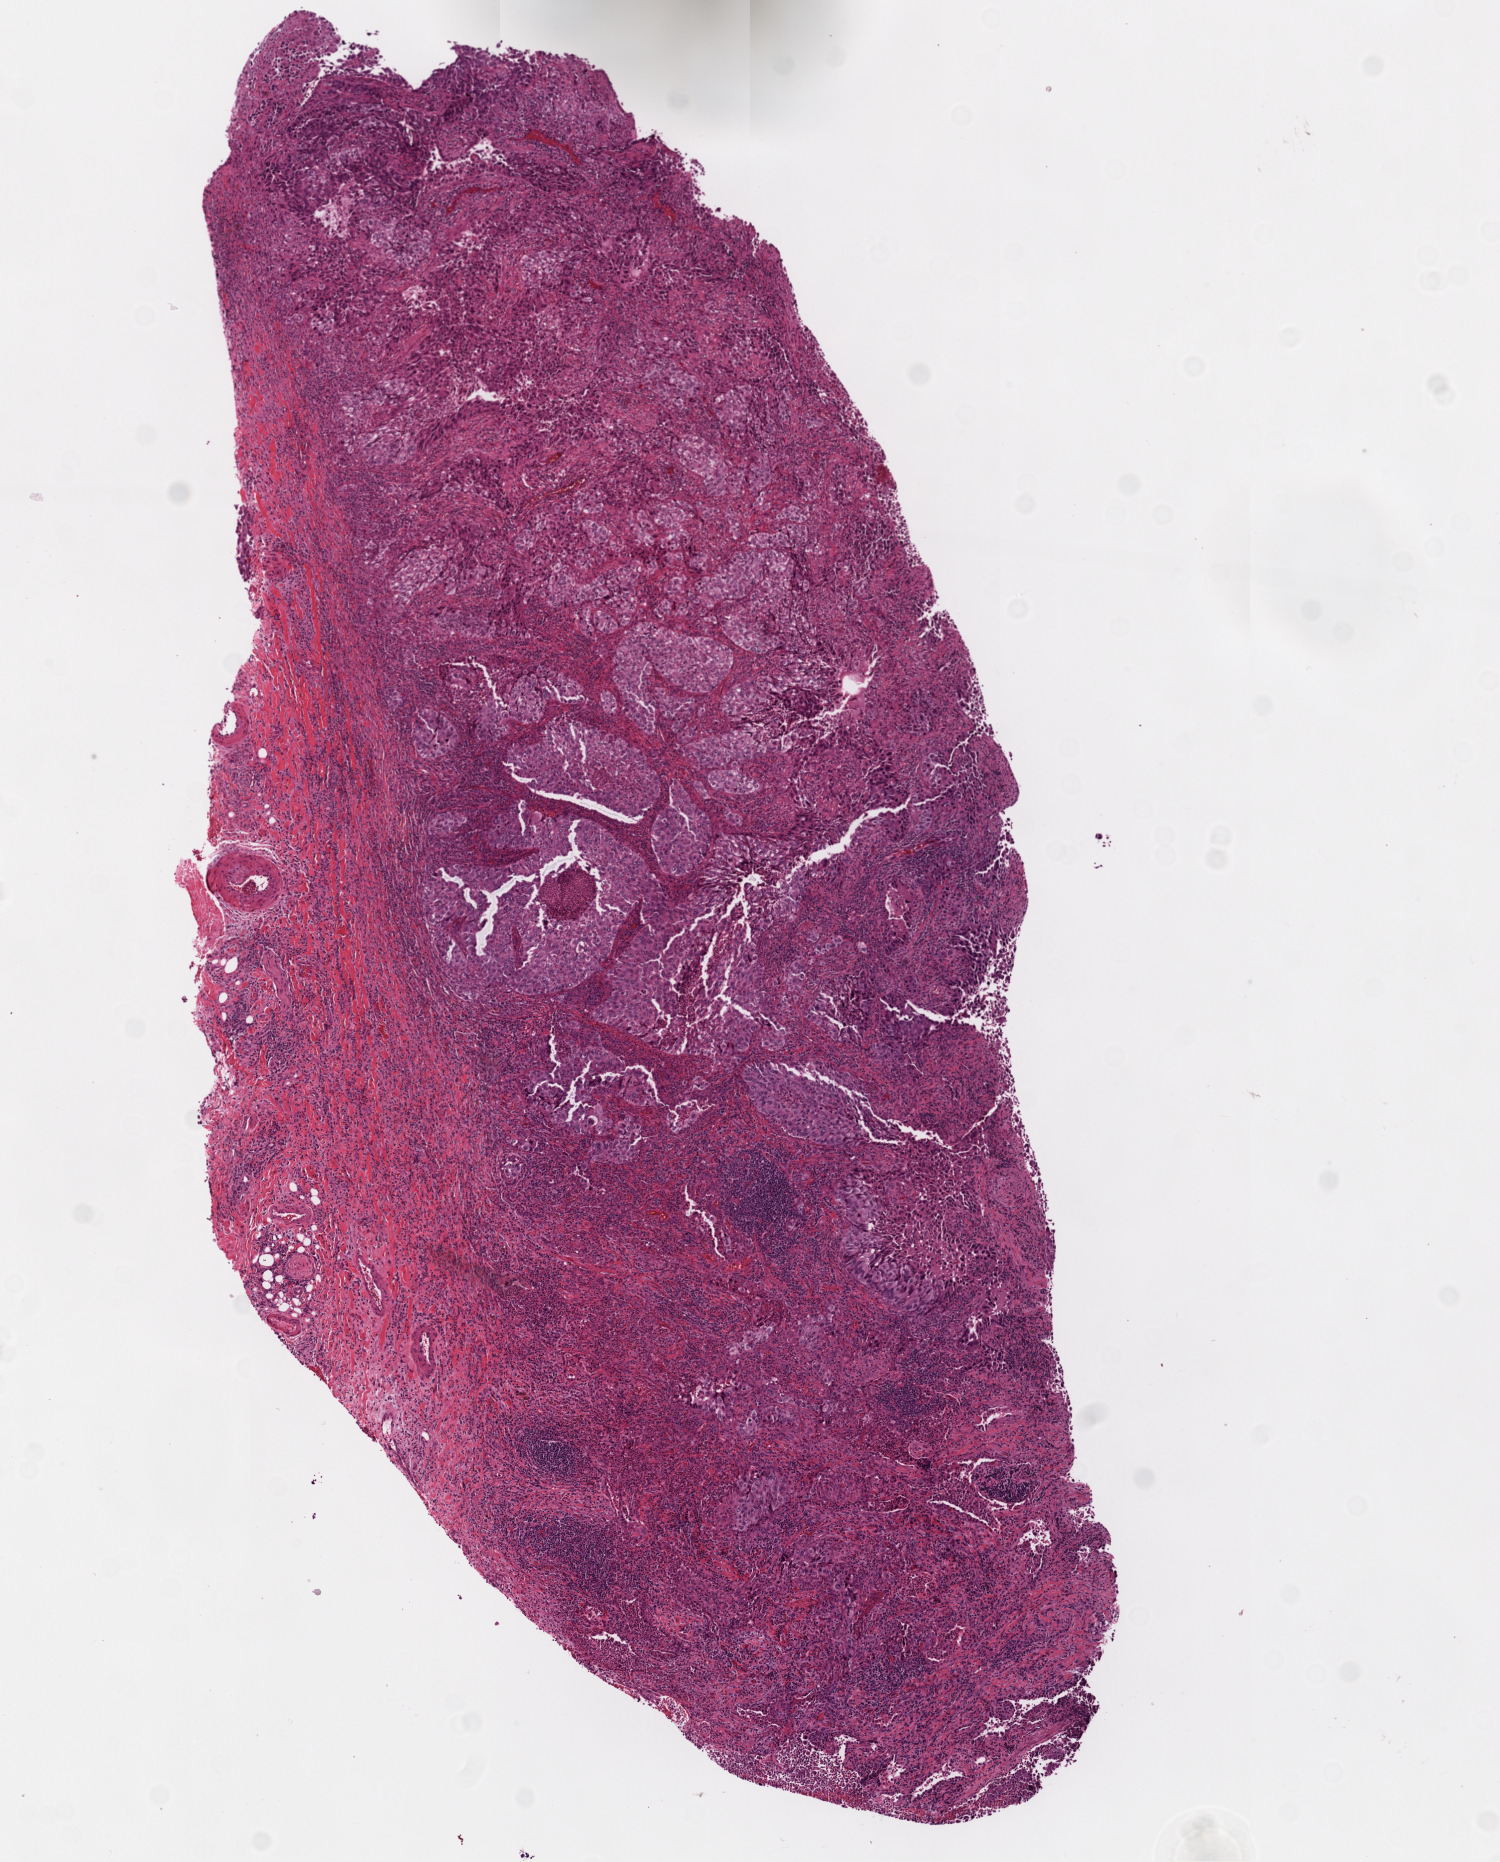
Digitized H&E tissue section (whole slide), shown as a low-resolution overview of the whole scanned area (about 6.0 x 7.5 mm, acquisition: 20x scan), frozen section from the top of the tissue portion, lung, primary tumour sample. Male, age 51 years at initial diagnosis. Slide review estimates, as recorded: tumour cells 70%, tumour nuclei 70%, normal cells 0%, stromal cells 30%, necrosis 0%. Infiltration values recorded for this section: lymphocyte infiltration 20%.
Pathologic diagnosis: Adenocarcinoma, NOS (upper lobe, lung). AJCC pathologic stage: IB.